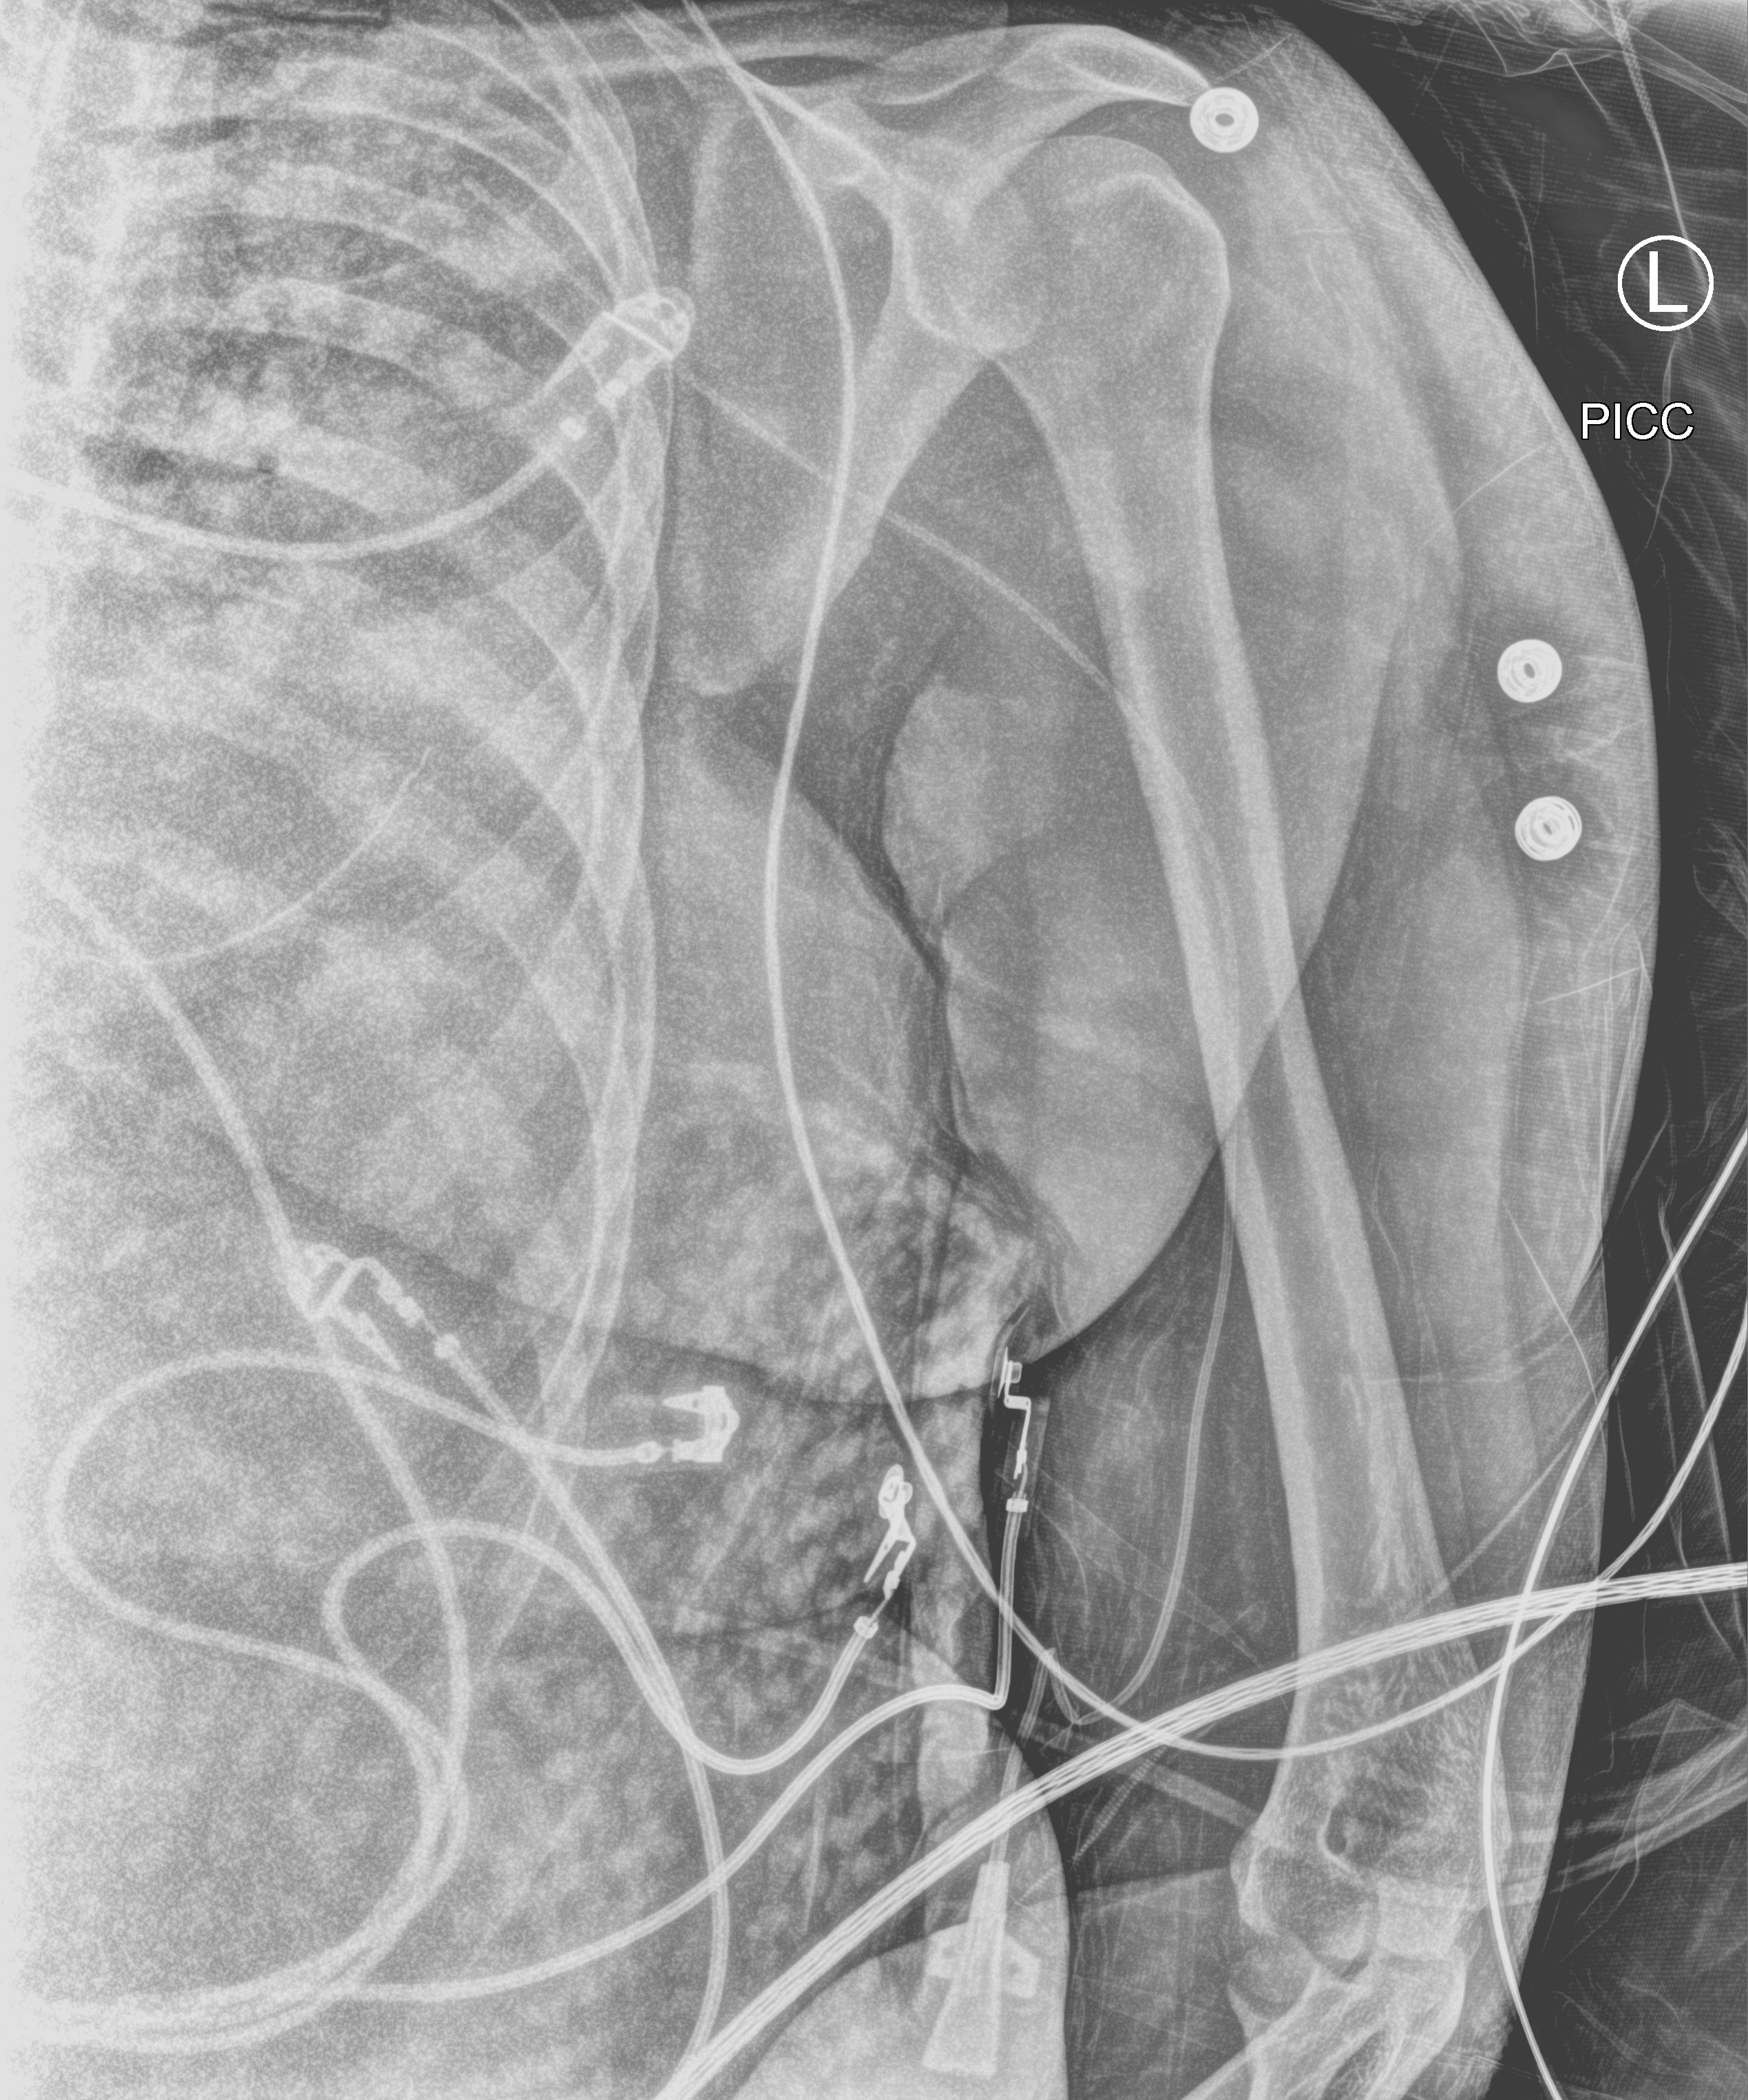
Bedside chest radiograph (computed radiography); anteroposterior (AP) projection. Adult patient hospitalised with COVID-19, age 18–59 years.
Admission-level facts for this patient (not findings on this image; timing relative to this image not recorded): other chronic lung disease (admission record): no; smoking status (admission record): never; admitted to intensive care during this hospital stay: yes.